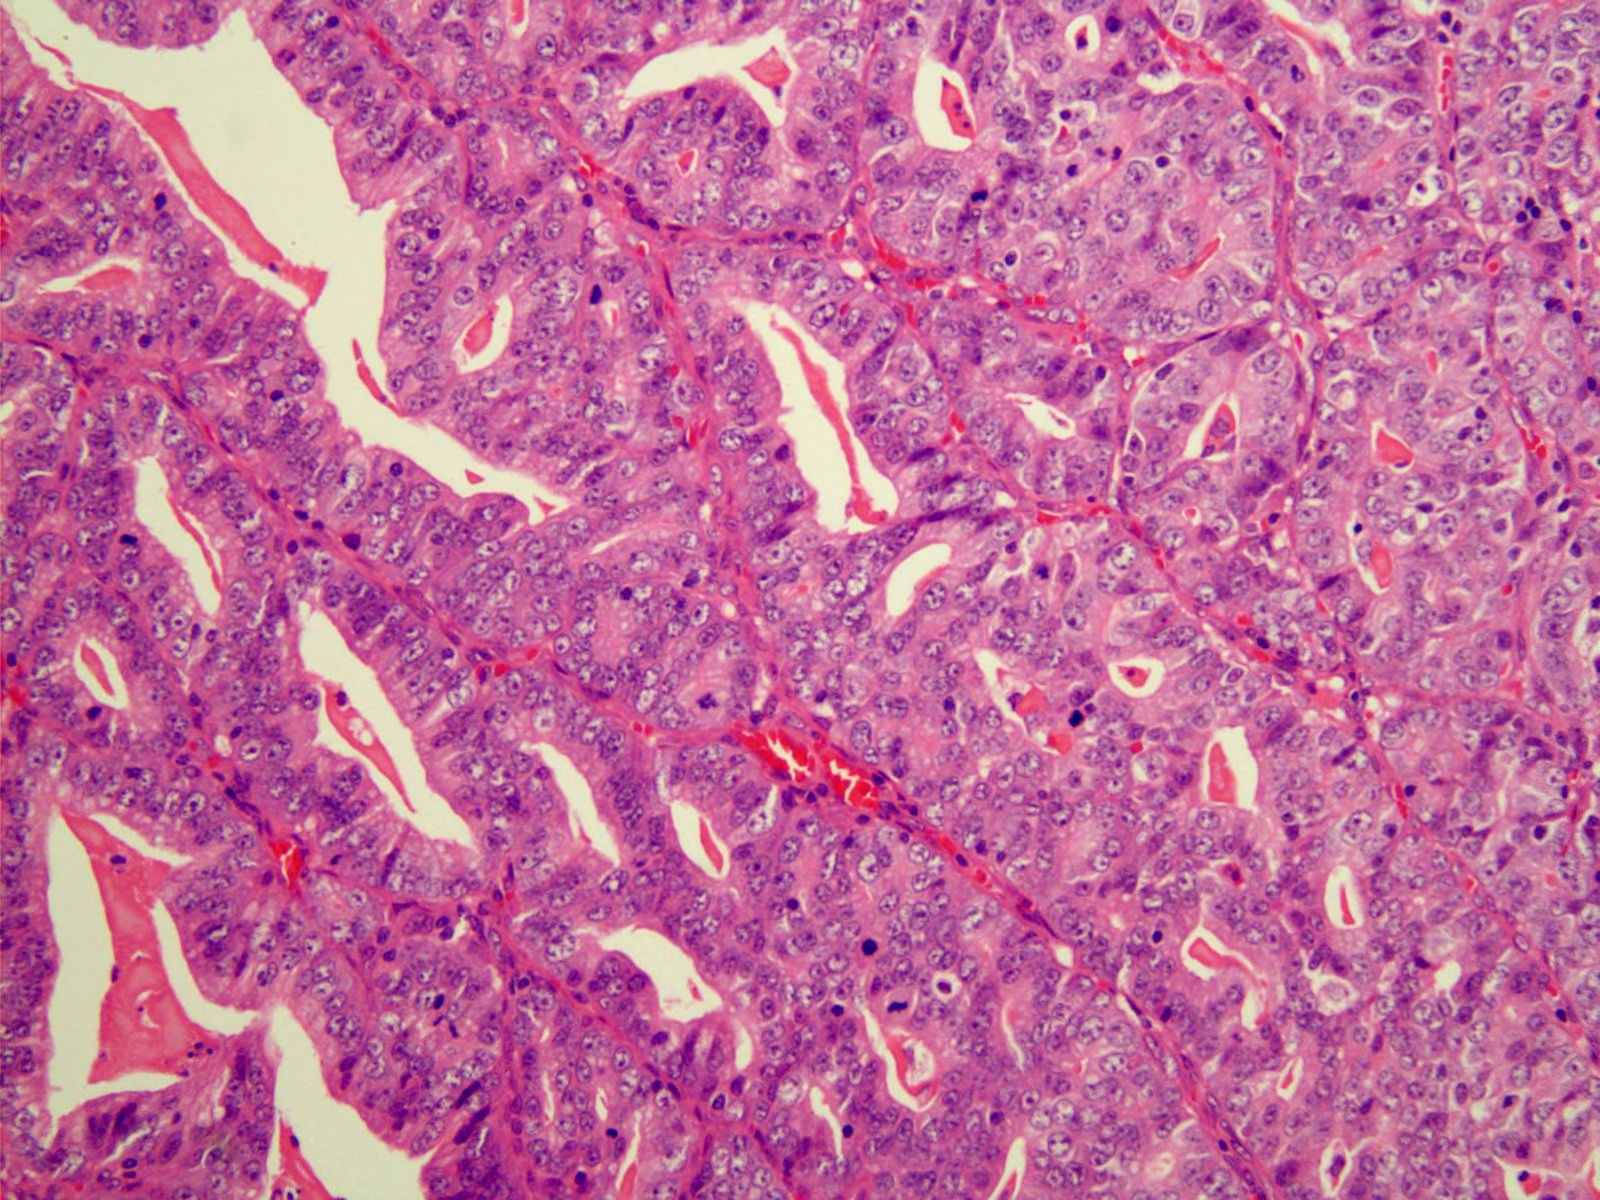
H&E-stained micrograph of a single small tissue field — covering about 0.8 x 0.6 mm. Formalin-fixed paraffin-embedded (FFPE) diagnostic section. Sample: primary tumour, stomach. Patient: male, age at initial diagnosis 72 years.
Pathologic diagnosis: Adenocarcinoma, NOS.